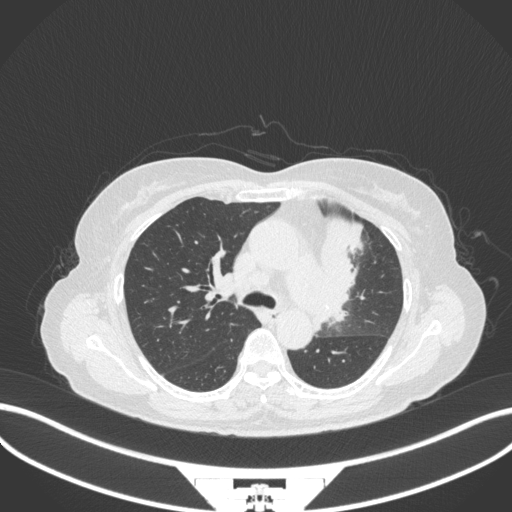
Chest CT, one axial slice; position 220 of 382 along the scan axis; reconstruction kernel B31f; lung window (W 1500 / L -600 HU); 1 mm slice thickness; 512 × 512 image matrix, field of view 400 × 400 mm. Female patient, age 64 years. Case-level facts recorded for this patient, not image findings: clinical TNM (as recorded): T2a N2 M0.
Outlined on this slice (bounding box drawn by a radiologist):
- lung tumour (recorded histology: adenocarcinoma): bounding box <315,214,367,332> (left, top, right, bottom; pixels)